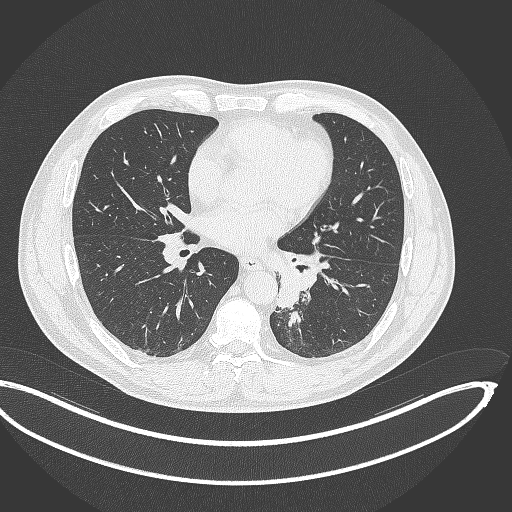
Chest CT, one axial slice; slice 165 of 362 in the series (ordered by position); 120 kVp; lung window (W 1500 / L -600 HU); 1 mm slice thickness; 512 × 512 image matrix, field of view 442 × 442 mm. Male patient, age 50 years. From the clinical record (not read from this slice): clinical TNM (as recorded): T2a N3 M0.
Structures marked on this image (rectangle marked by the reading radiologist):
- lung tumour (recorded histology: squamous cell carcinoma): box from (x=272, y=262) to (x=314, y=311) px